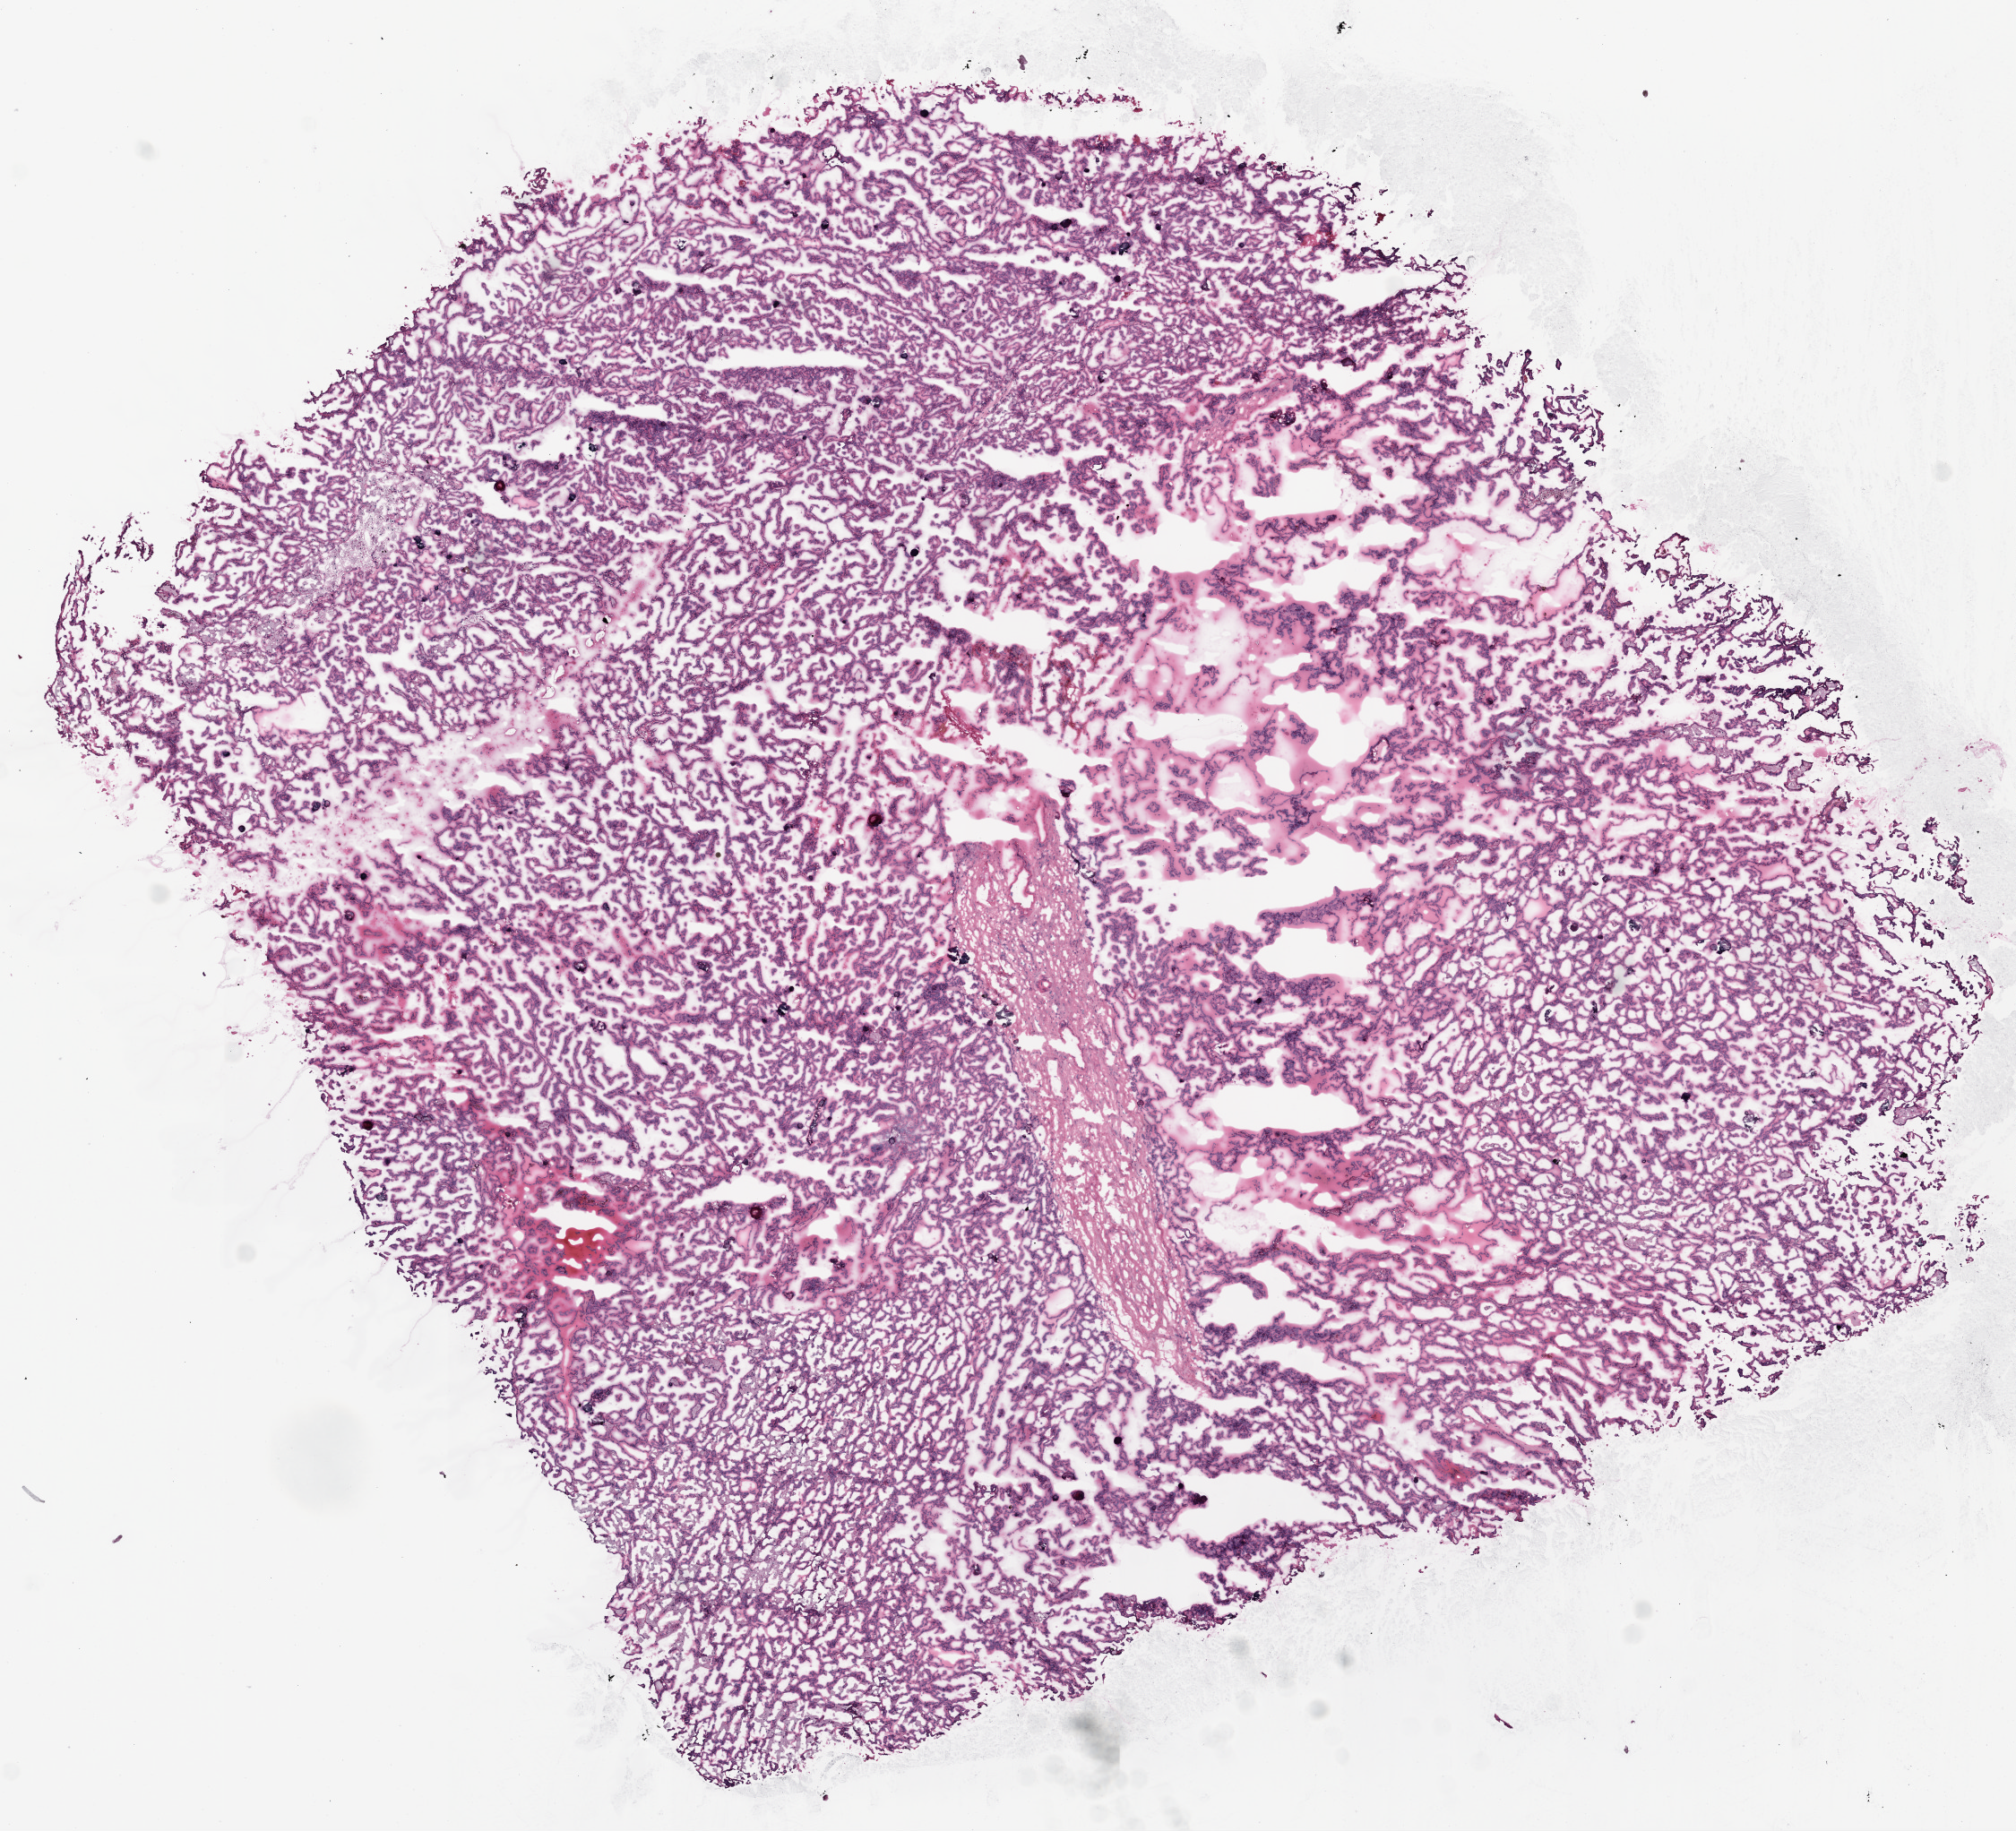
H&E whole-slide image — whole scanned area (about 9.0 x 8.2 mm, from a 20x scan) shown as a low-resolution overview. Frozen section from the top of the tissue portion. Primary tumour sample from the kidney. Male, age 74 years at initial diagnosis. Pathologist review of this section (percent, as recorded): tumour cells 82%, tumour nuclei 80%, normal cells 0%, stromal cells 10%, necrosis 8%.
* TNM: T1b NX M0
* AJCC pathologic stage: I (6th edition)
* histologic diagnosis: Papillary adenocarcinoma, NOS